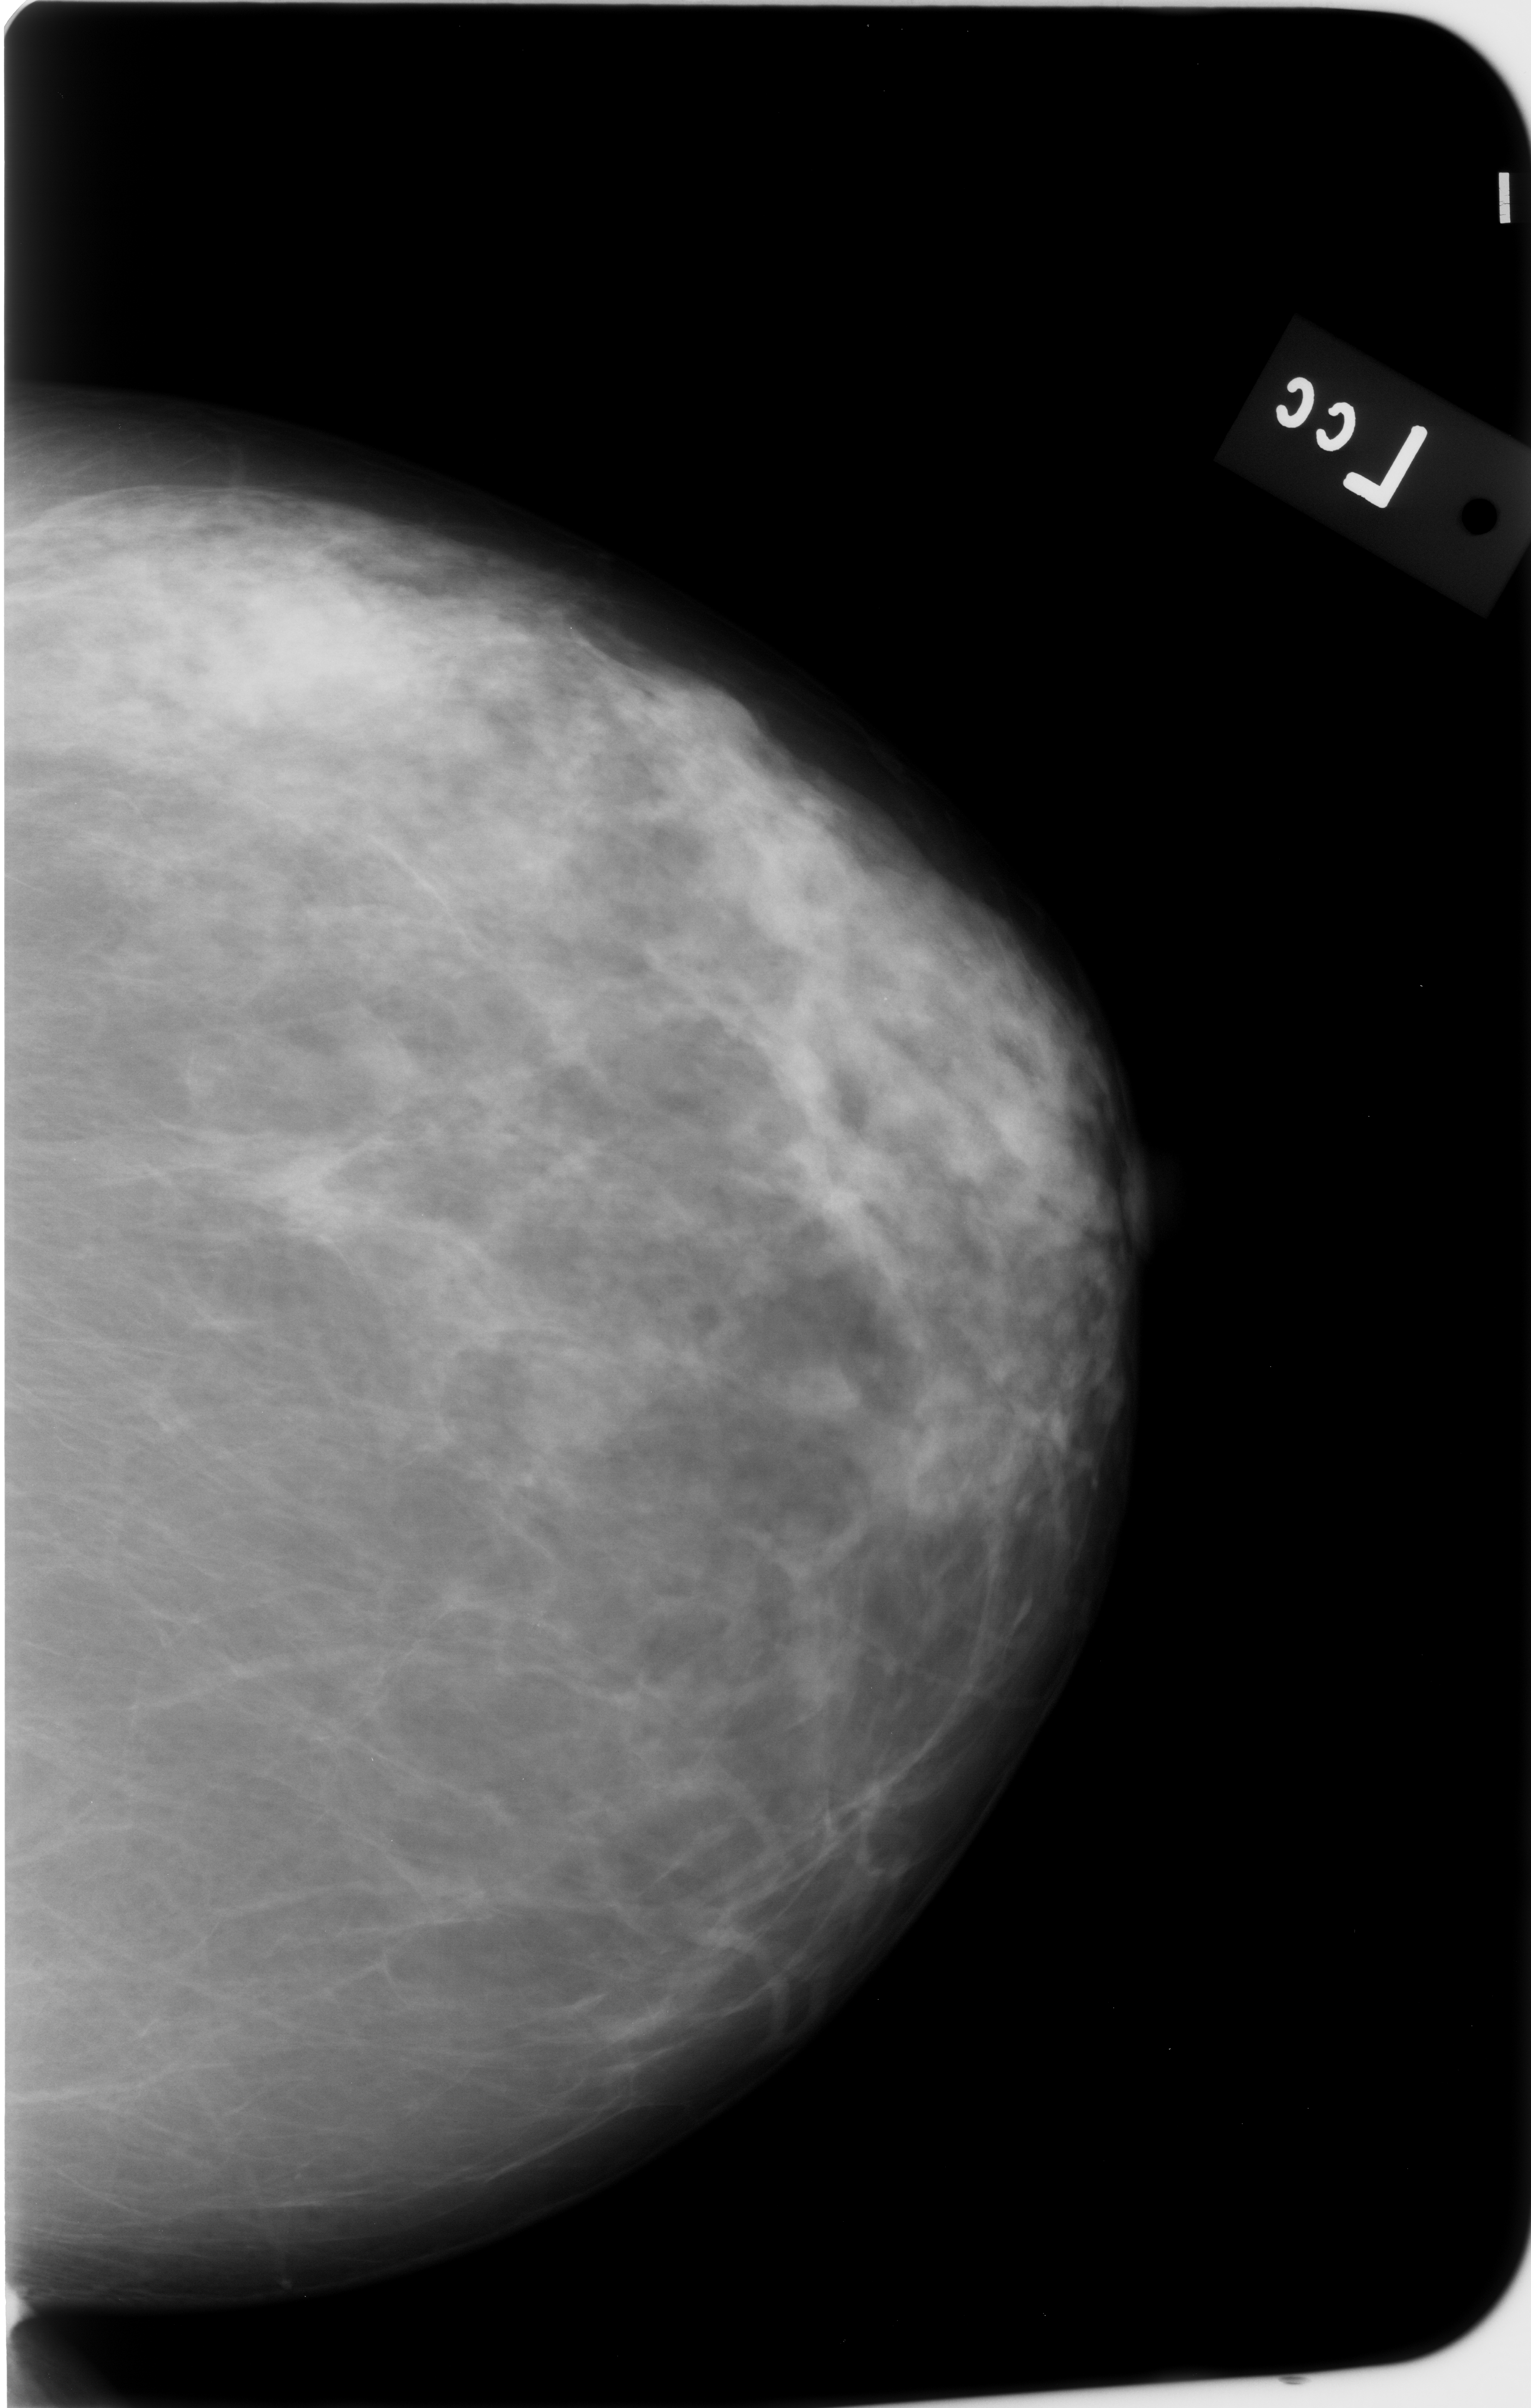
Mammogram (digitized film); left breast; craniocaudal (CC) view; breast composition: scattered fibroglandular densities (BI-RADS density category 2 of 4).
Calcifications, morphology pleomorphic, distribution clustered; BI-RADS assessment category 4; pathology (as recorded): benign.